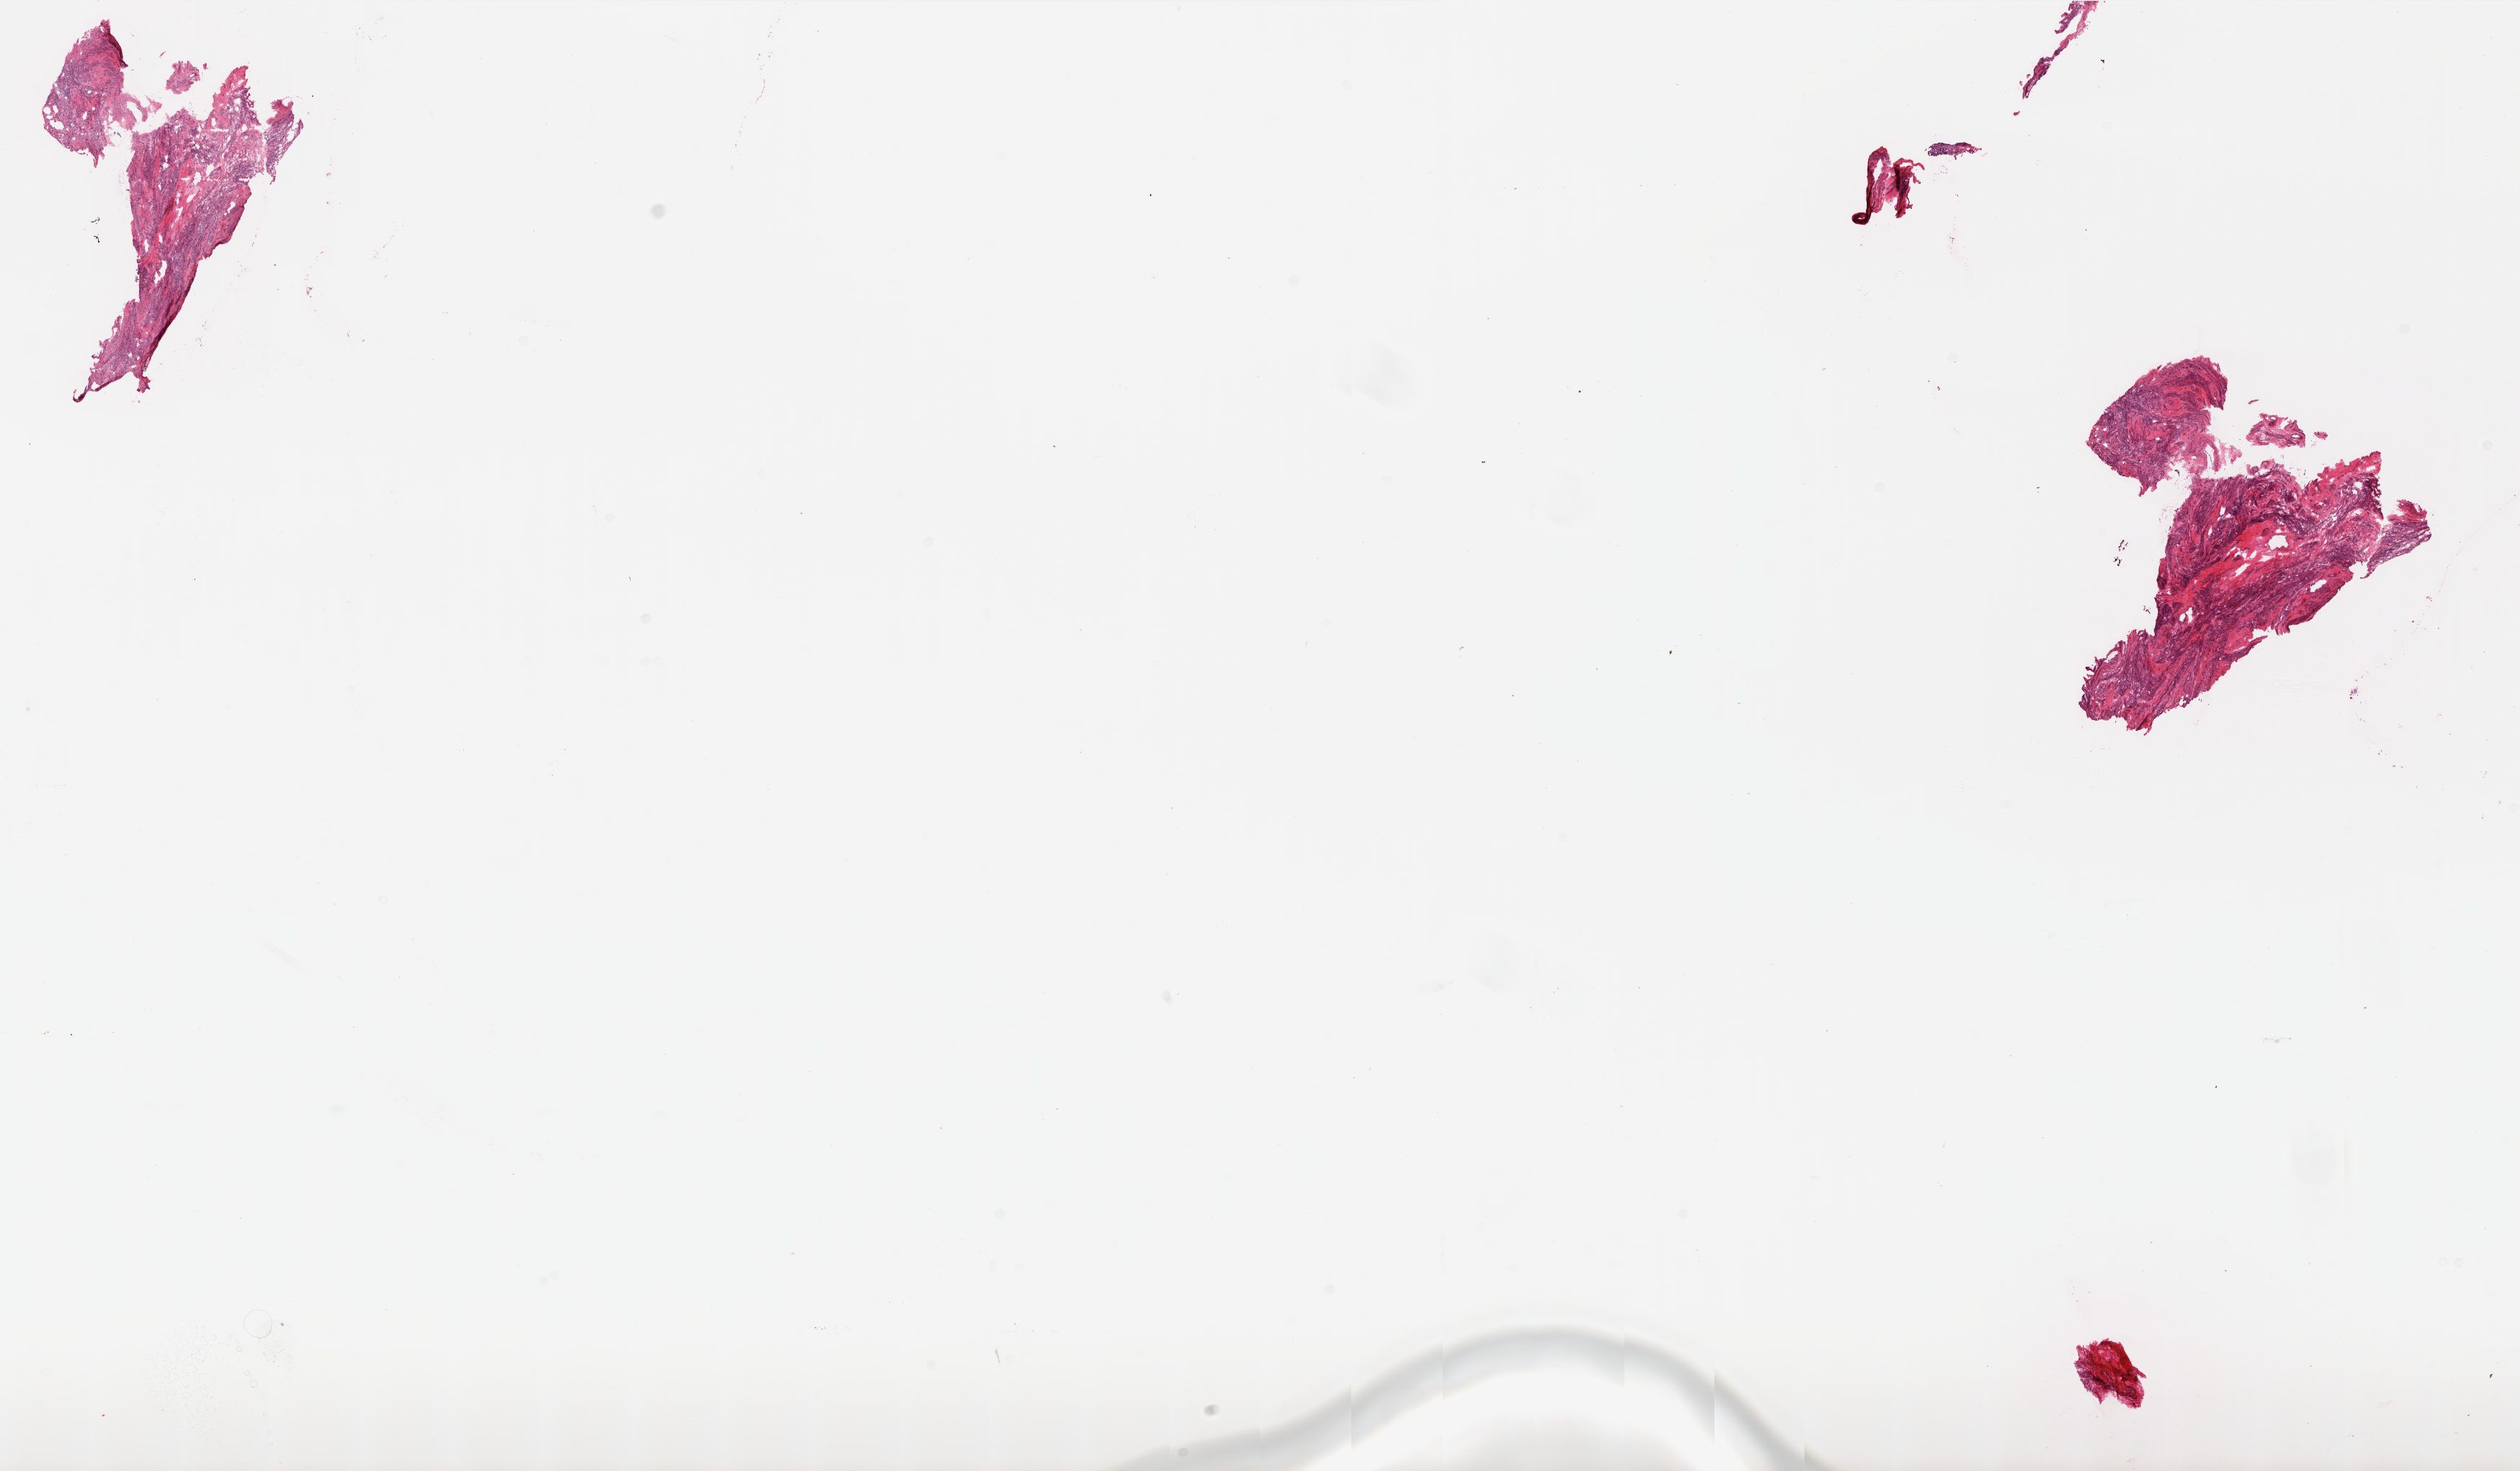
Digitized H&E-stained tissue section (whole slide) — shown as a low-resolution overview of the whole scanned area (about 27.9 x 16.3 mm, from a 20x scan); frozen section from the top of the tissue portion; sample: solid tissue normal (non-tumour tissue), ovary. Female, age 60 years at initial diagnosis.
This section: solid tissue normal sample (biorepository sample class). Patient diagnosis: Serous cystadenocarcinoma, NOS.